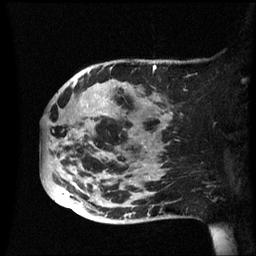
Breast MRI (dynamic contrast-enhanced), one sagittal slice. Position 21 of 60 along the scan axis. Dynamic contrast-enhanced series, image 2 of 3 at this slice position (ordered by acquisition). 1.5 T. TE 4.2 ms, TR 8.4 ms. 2.4 mm slice thickness. 256 × 256 image matrix, field of view 230 × 230 mm. Female patient, age 49 years.
Structures marked on this image (semi-automatically segmented with operator editing):
- analysis volume of interest (the breast-tissue region the enhancement analysis was run in; not a lesion): bounding box [x1, y1, x2, y2] px = [40, 59, 174, 224]
- tumour enhancement mask (voxels above the 70 % enhancement threshold inside the analysis volume of interest): [70, 65, 157, 221]